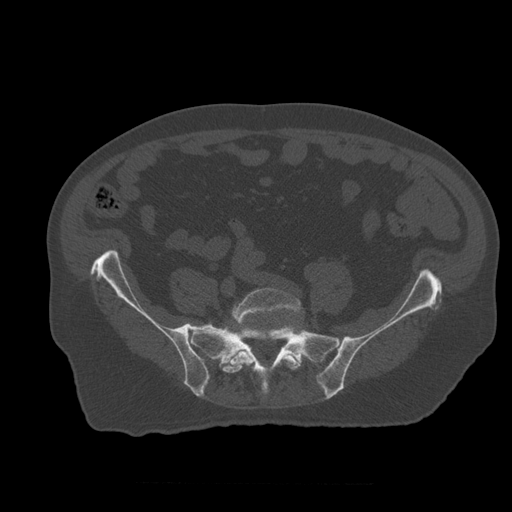
CT including the spine, one axial slice; position 130 of 399 along the scan axis; bone window (W 1800 / L 400 HU); 1.25 mm slice thickness; 512 × 512 image matrix, field of view 407 × 407 mm. Patient age 73 years. From the clinical record (not read from this slice): primary cancer: prostate; vertebrae with lytic lesions (as recorded): L2.
Structures marked on this image (semi-automatically segmented with operator editing):
- L5 vertebra: bounding box [x1, y1, x2, y2] px = [223, 288, 302, 373]